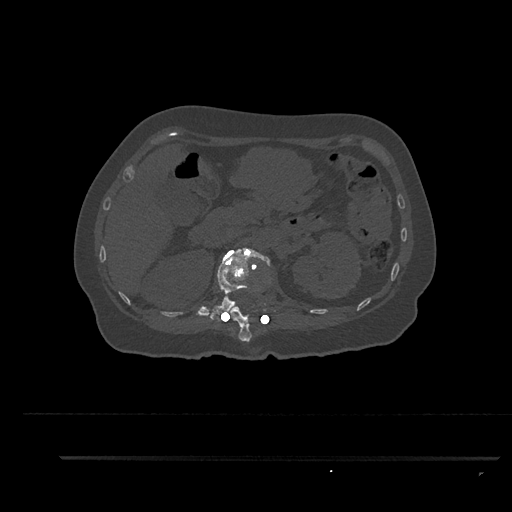
CT including the spine, one axial slice. Position 234 of 797 along the scan axis. Reconstruction kernel Br40s/3. Bone window (W 1800 / L 400 HU). 512 × 512 image matrix, field of view 408 × 408 mm. Patient: female, 44 years. From the clinical record (not read from this slice): primary cancer: renal; vertebrae with lytic lesions (as recorded): L1.
Outlined on this slice (semi-automatic segmentation, software-assisted and operator-edited):
- L1 vertebra: box from (x=209, y=248) to (x=271, y=322) px
- T12 vertebra: (x=217, y=307)–(x=258, y=342)